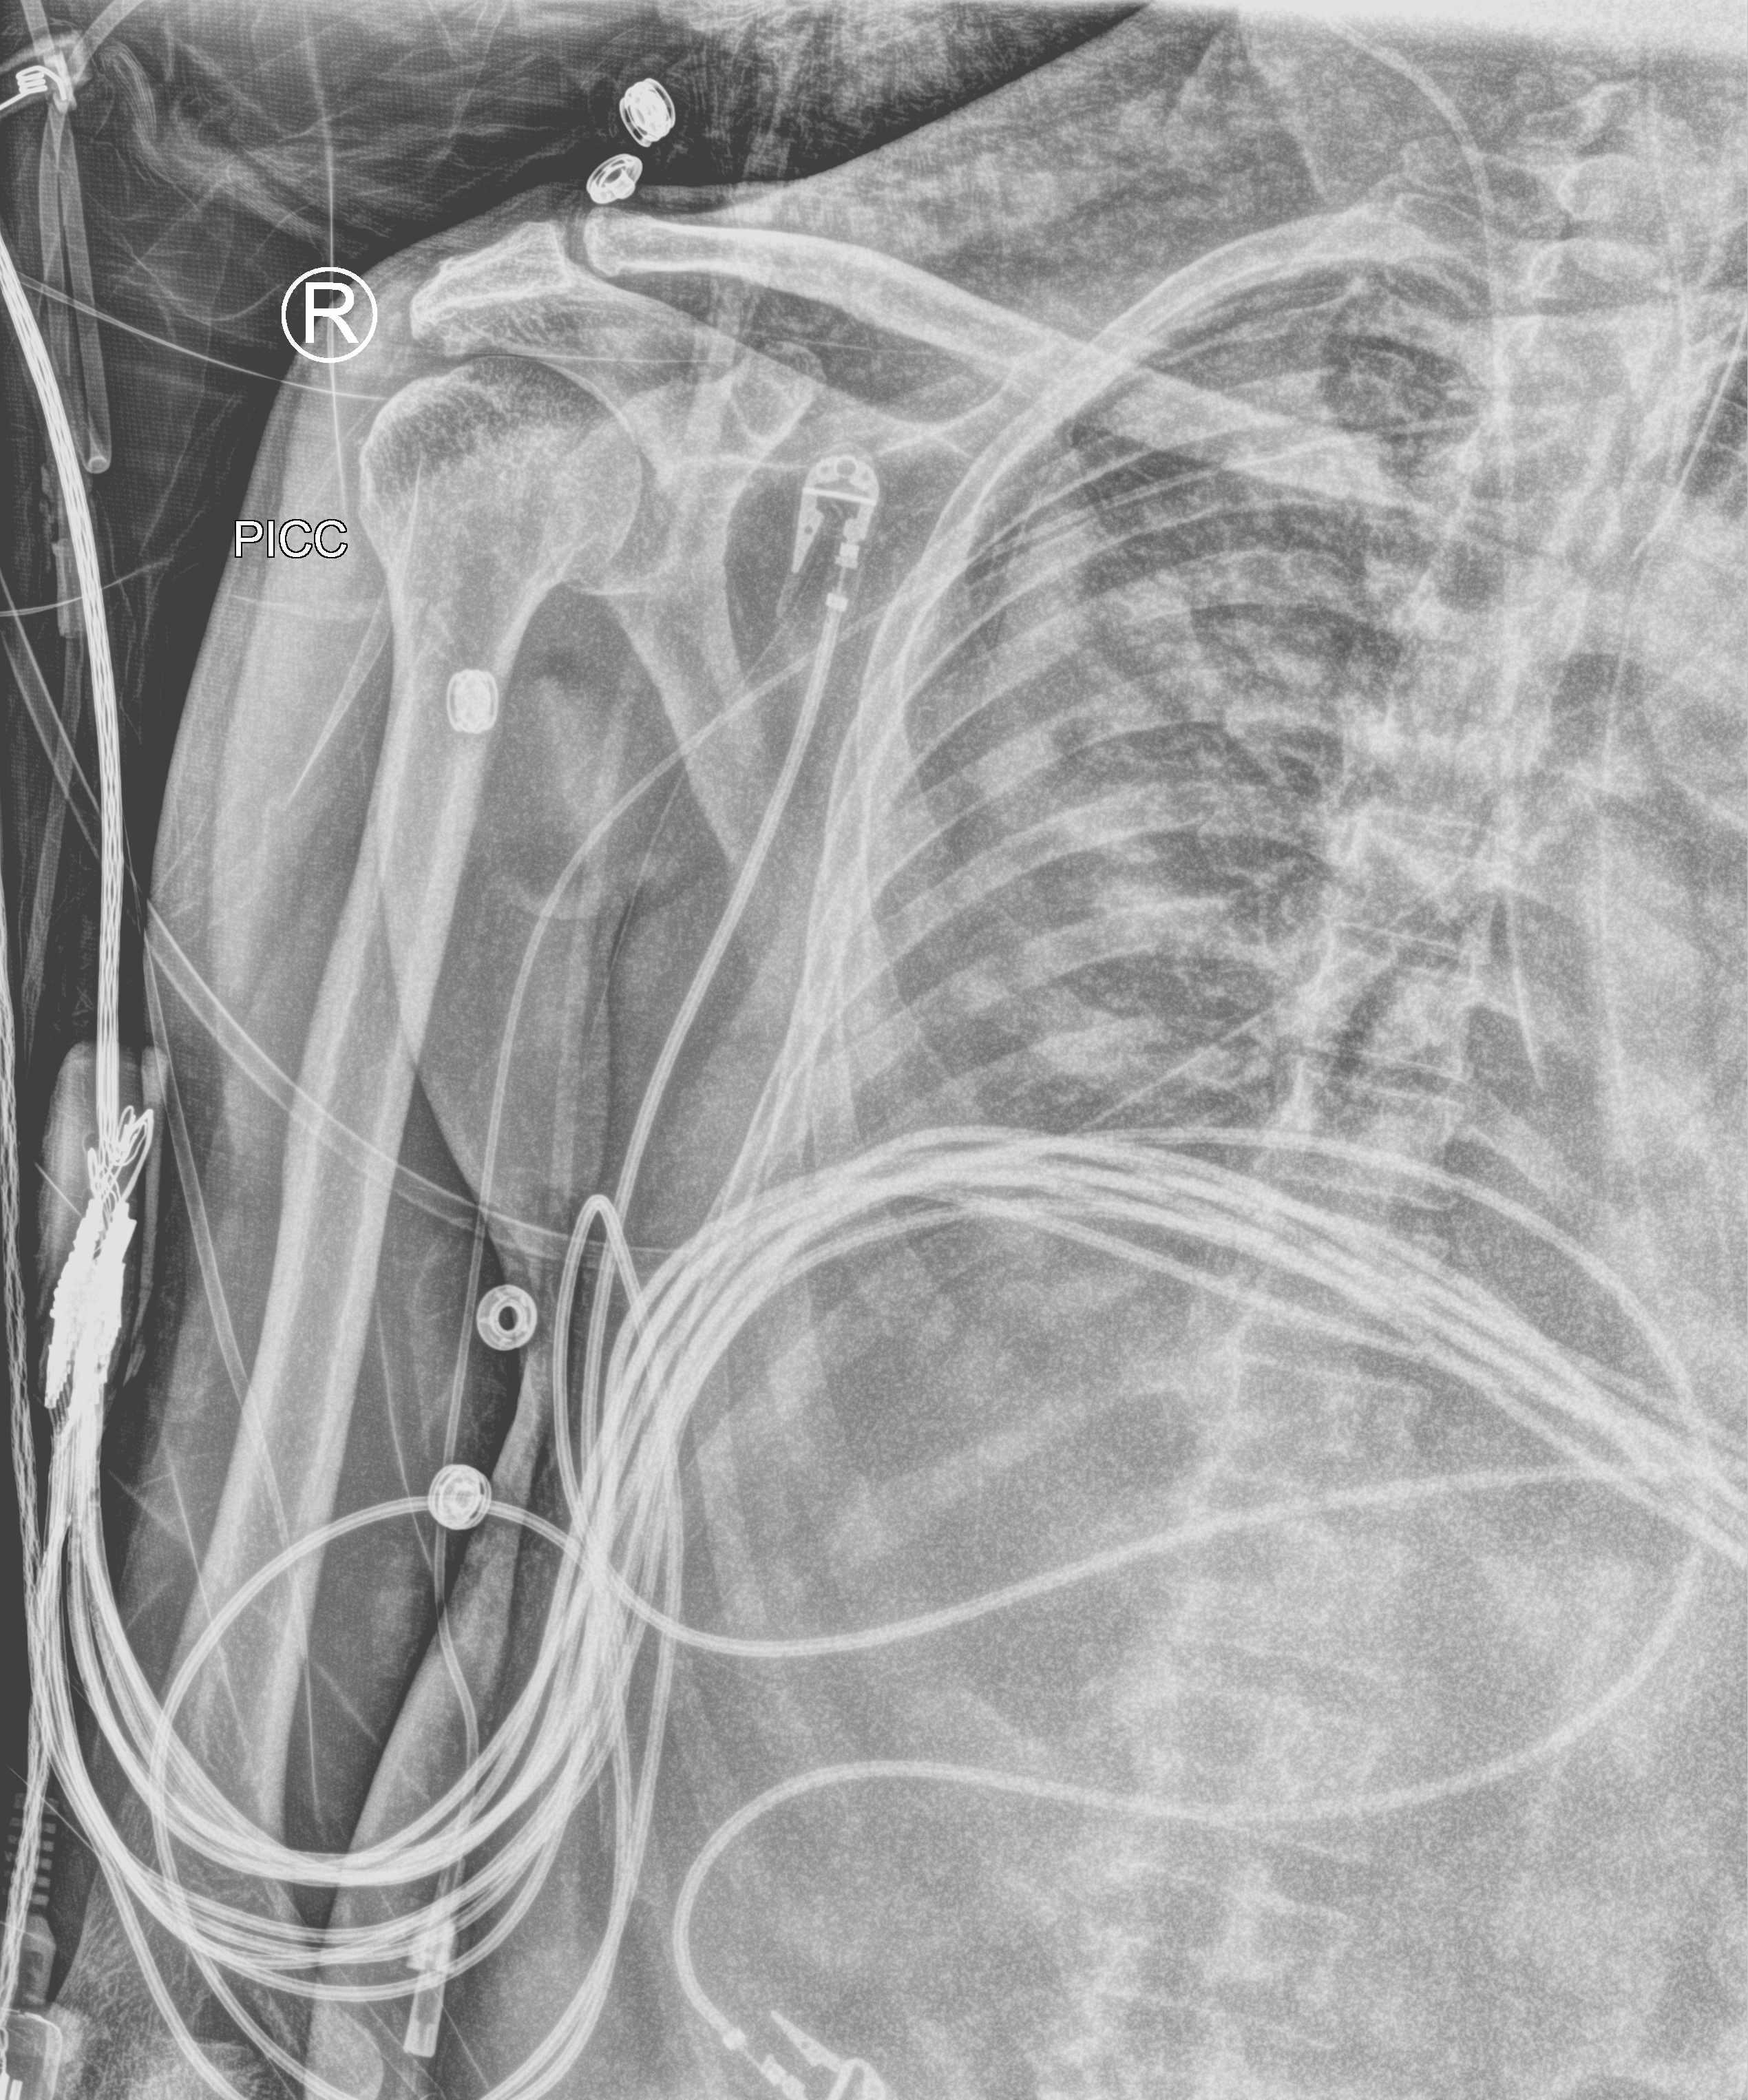
Chest X-ray (portable). Male patient hospitalised with COVID-19, age 18–59 years.
Hospital-stay facts (about this admission, not read from this image; timing relative to this image not recorded):
- admitted to intensive care during this hospital stay: yes
- mechanically ventilated during this hospital stay: yes